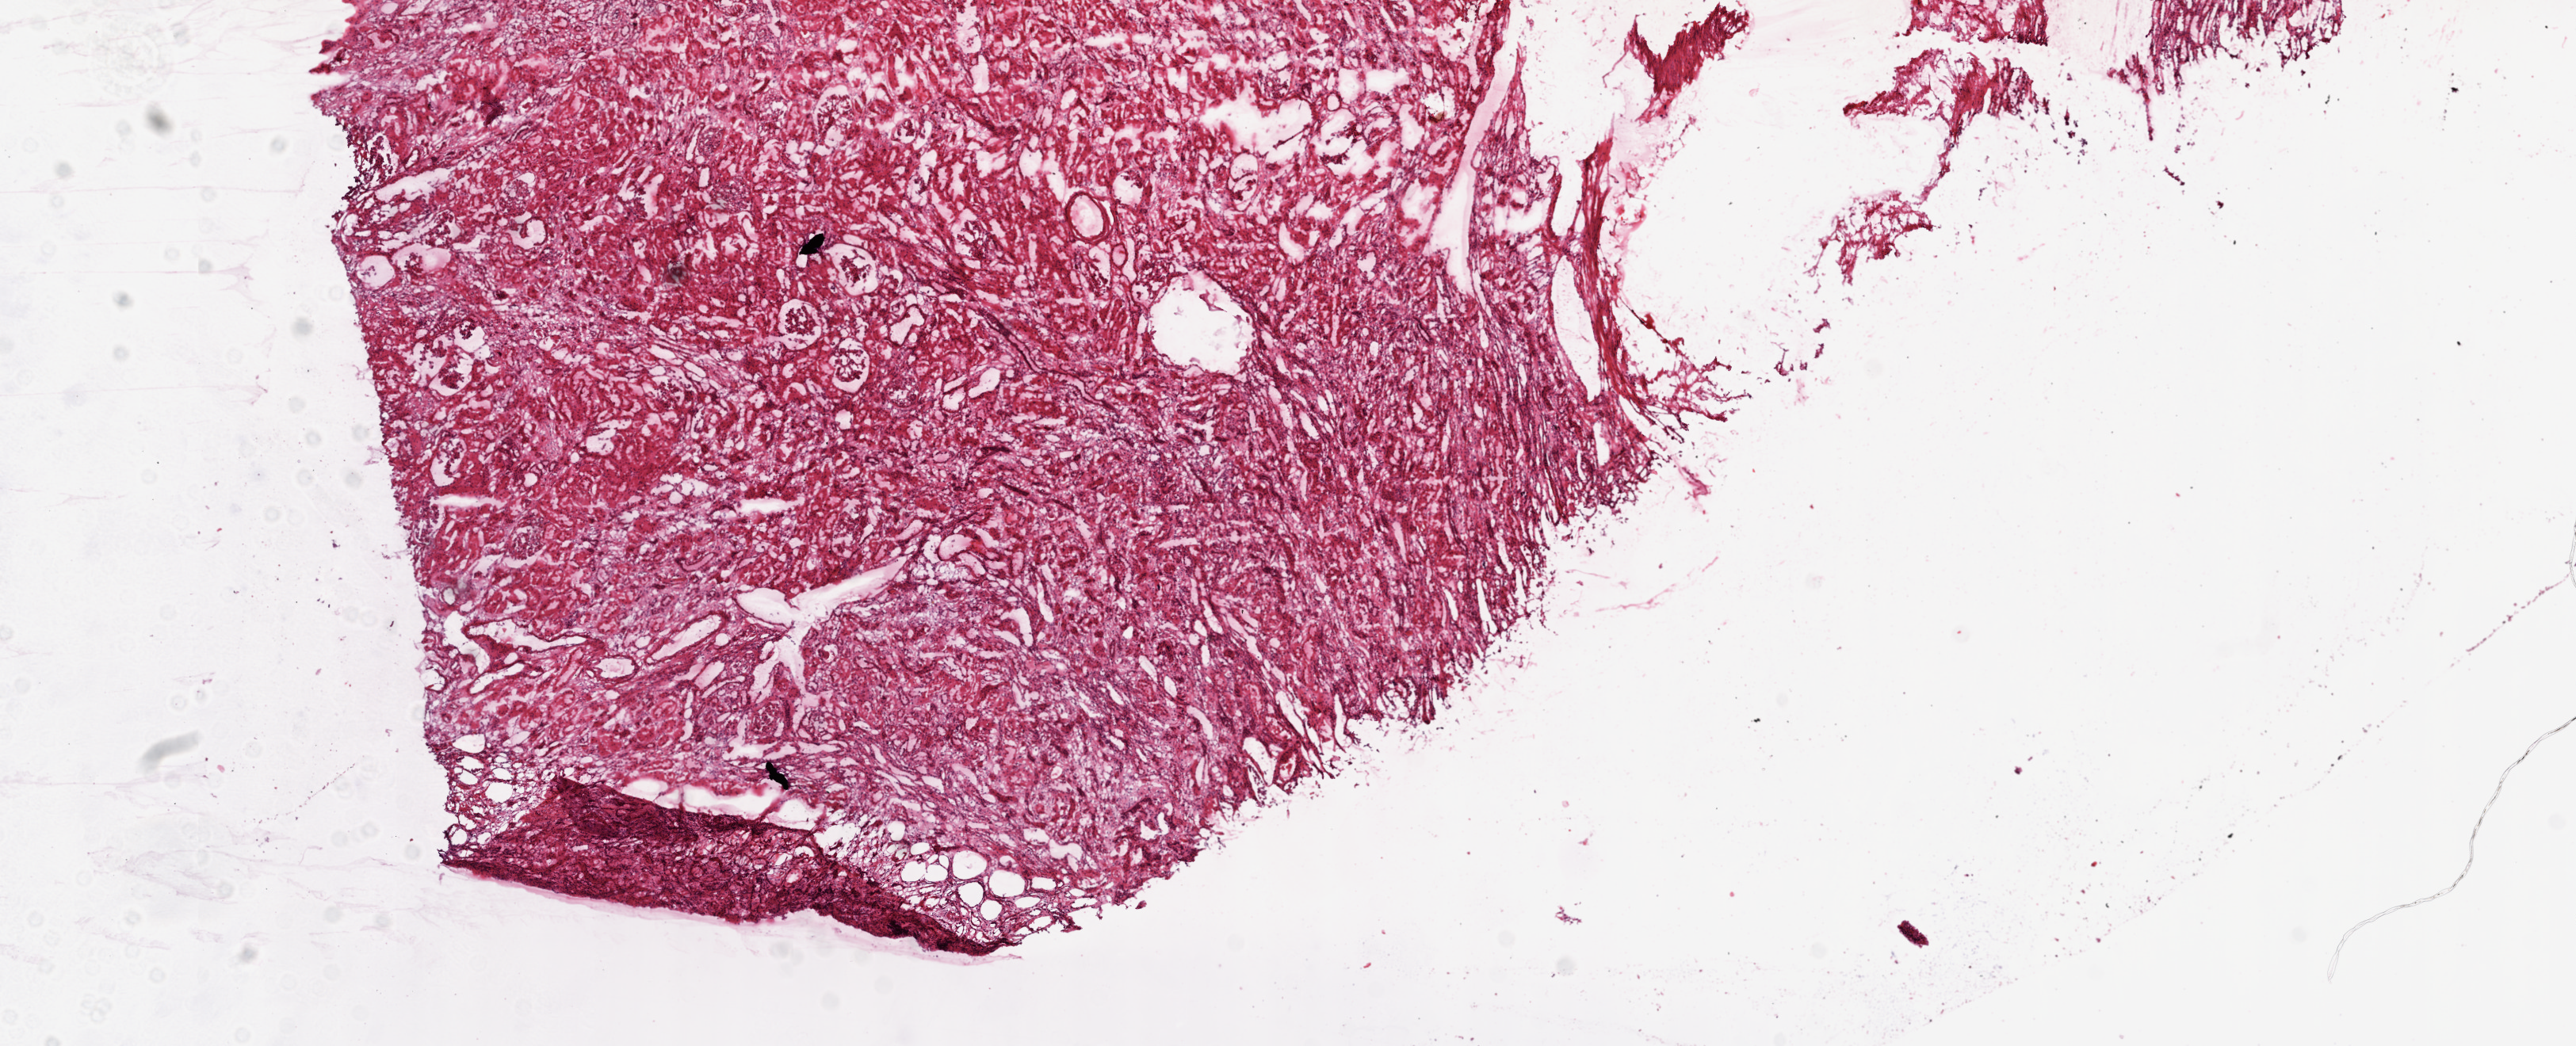
Whole-slide histology image, H&E-stained — a low-resolution overview of the entire scanned area, about 13.0 x 5.3 mm (from a 20x scan); frozen section; sample: solid tissue normal (non-tumour tissue), kidney. Patient: female, age at initial diagnosis 88 years.
This section: solid tissue normal (non-tumour) sample from the same patient. Patient diagnosis: Clear cell adenocarcinoma, NOS.